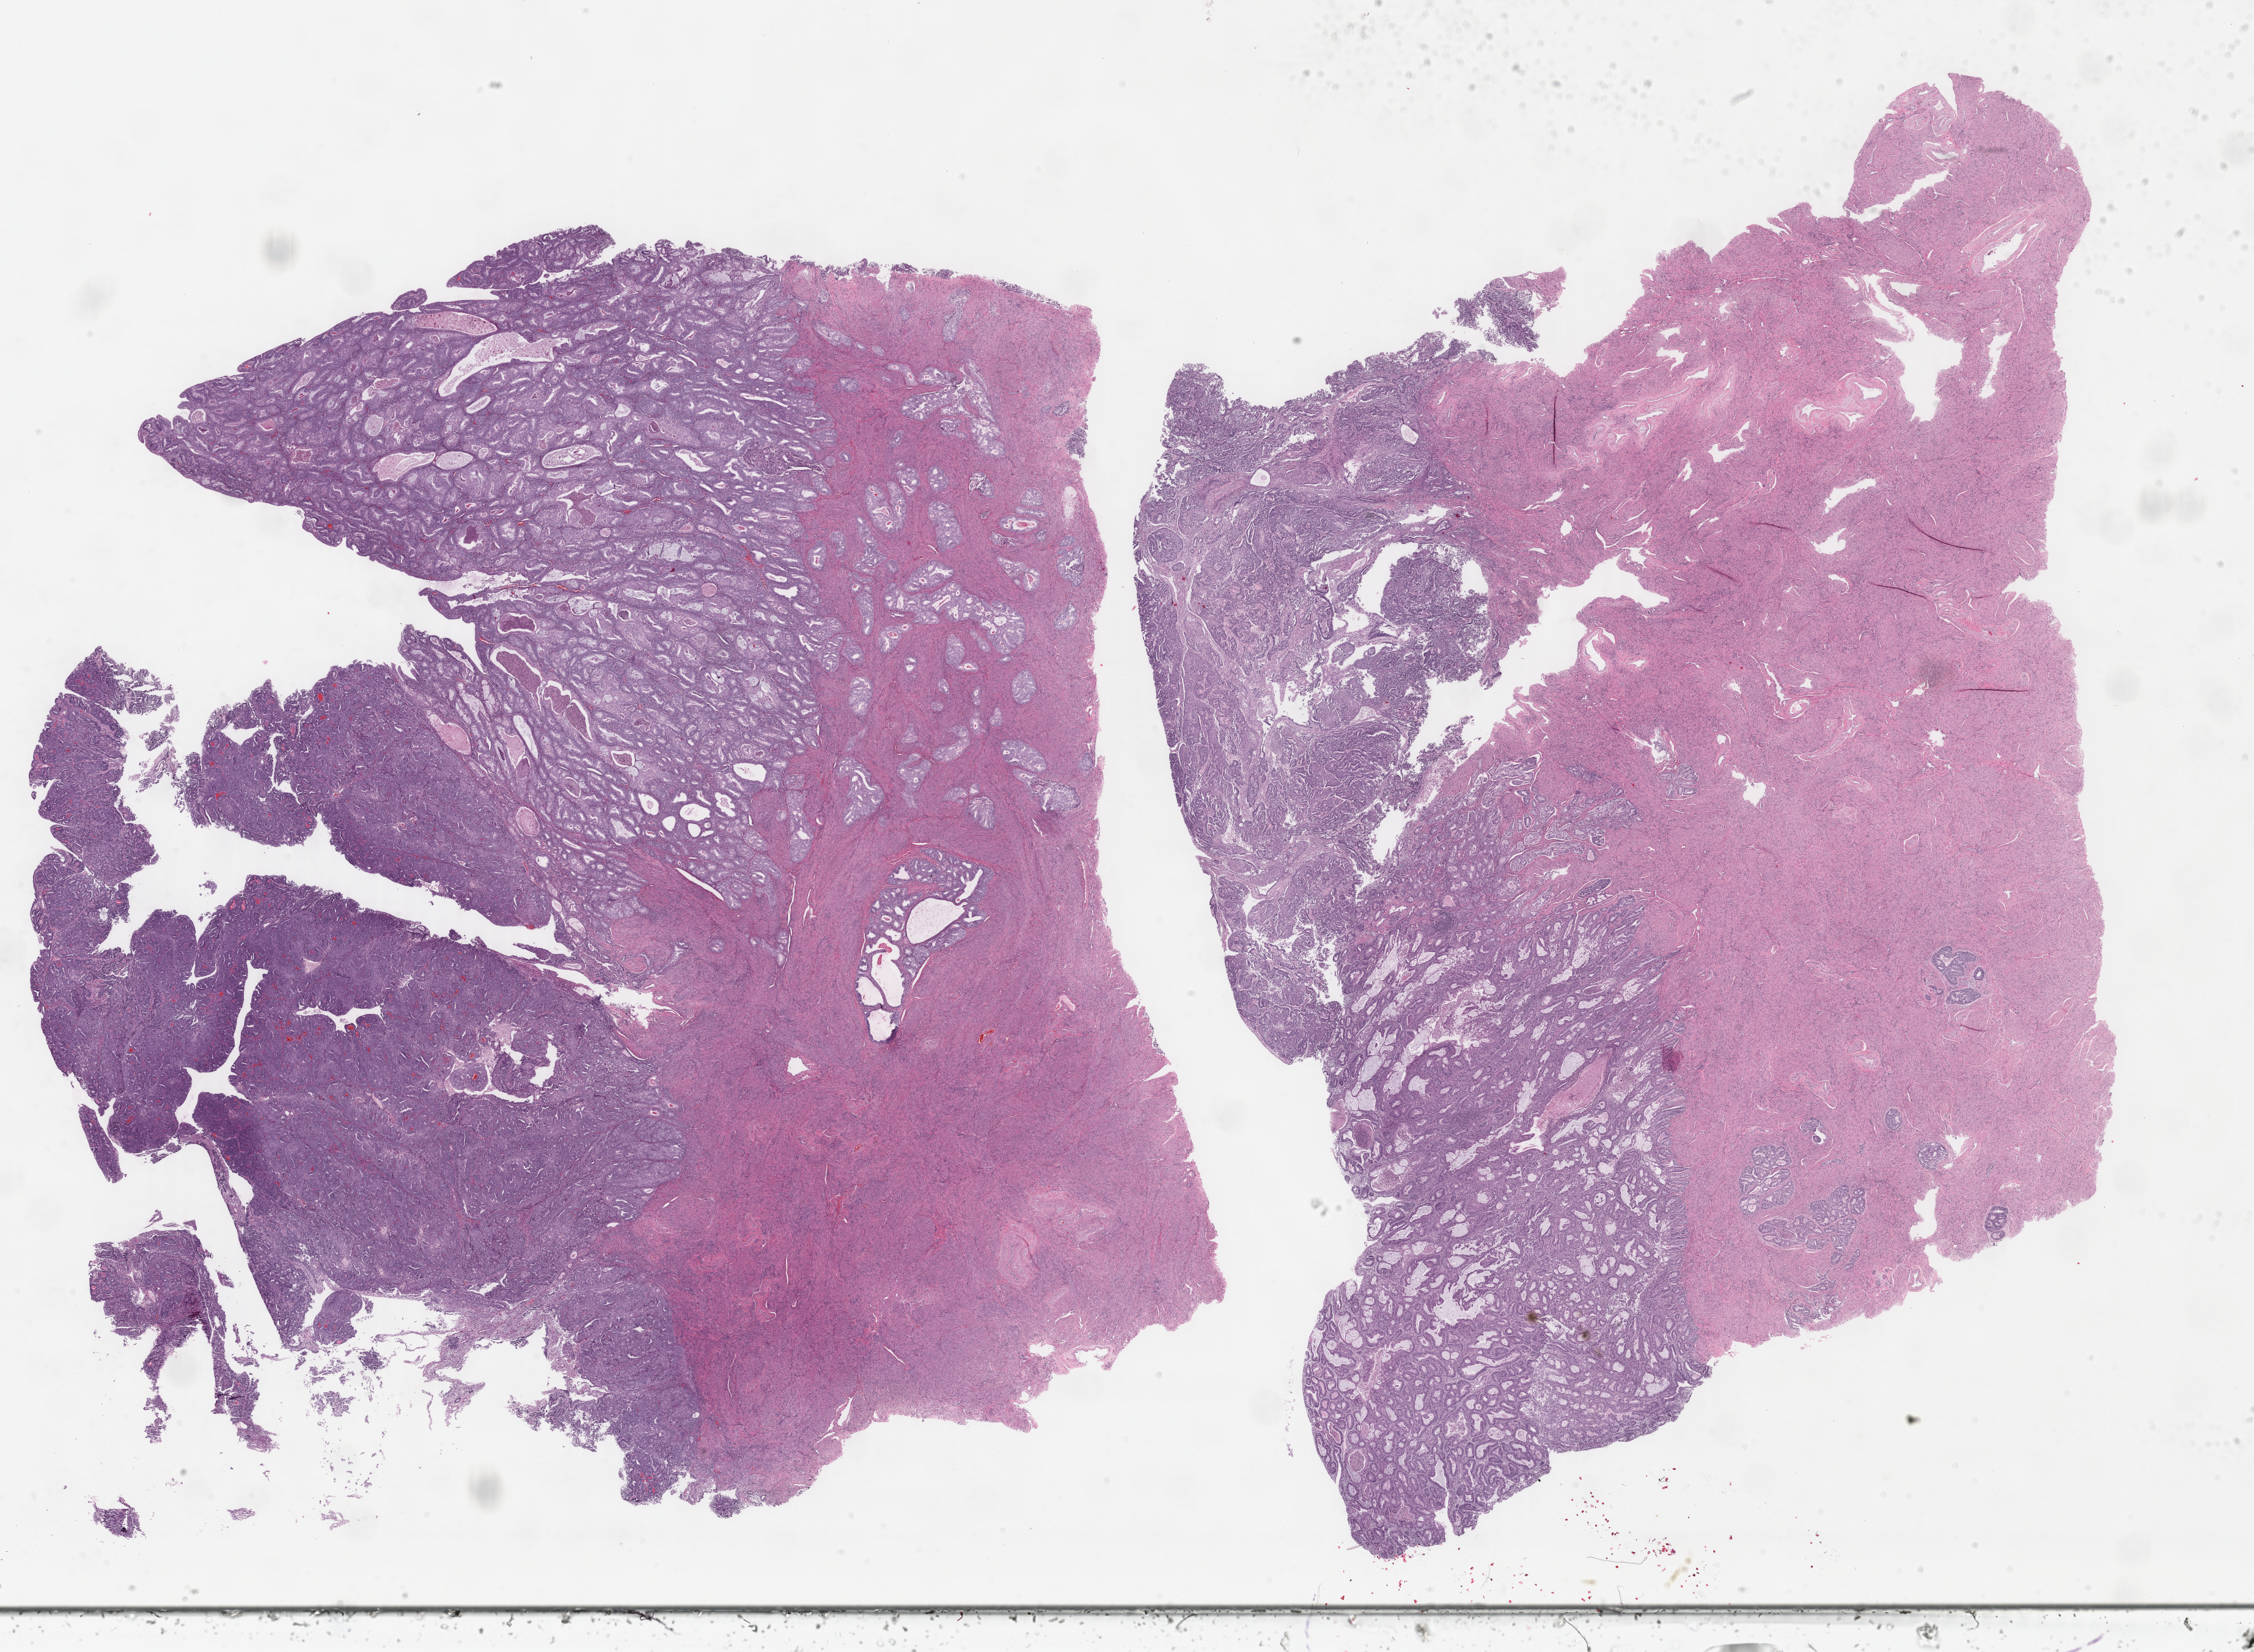
Hematoxylin and eosin (H&E) stained whole-slide image — whole scanned area (about 29.3 x 21.5 mm, acquisition: 40x scan) shown as a low-resolution overview; formalin-fixed paraffin-embedded (FFPE) diagnostic section; sample: primary tumour, uterus. Female, age 72 years at initial diagnosis.
Diagnosis: Endometrioid adenocarcinoma, NOS.